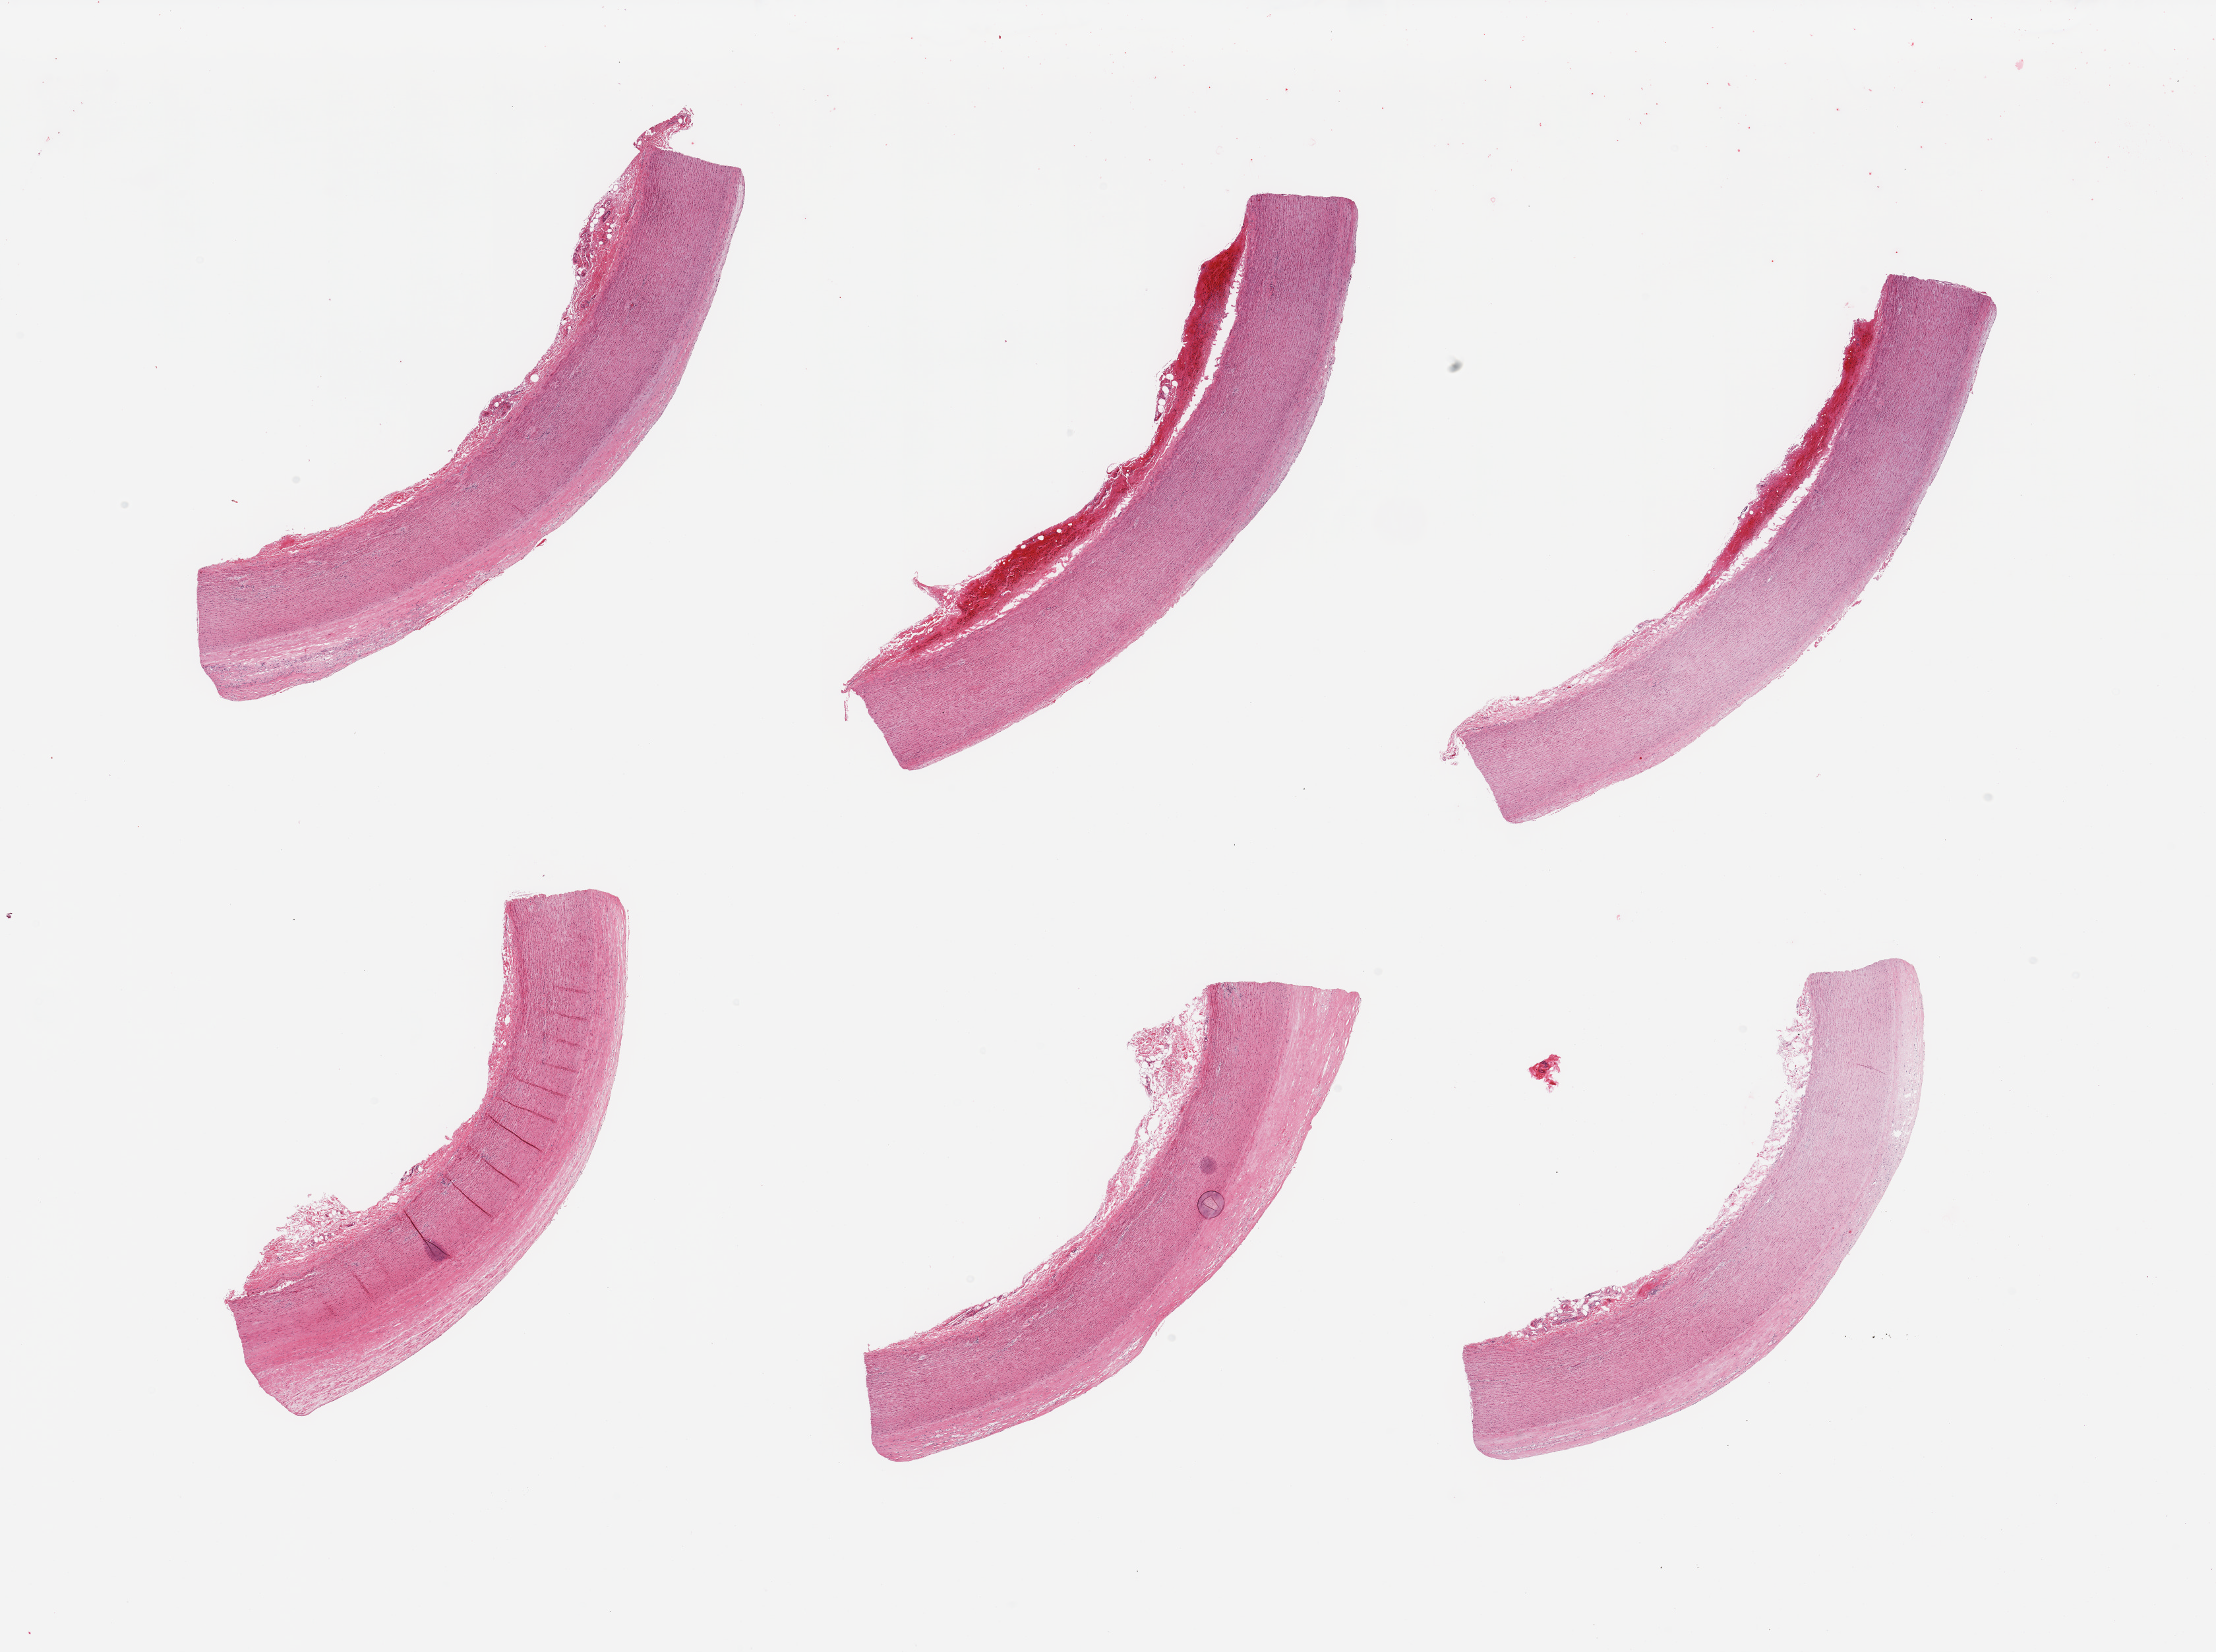
H&E whole-slide image, low-resolution overview of the scanned area, about 26.6 x 19.8 mm (acquisition: 20x scan); PAXgene-fixed, paraffin-embedded tissue; sampled site (target tissue): aorta; tissue donor sample. Donor: female.
- review note (as recorded): 6 pieces; flat plaques up to 0.6 mm